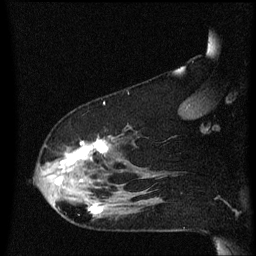
Breast MRI (dynamic contrast-enhanced), one sagittal slice. Slice 46 of 60 in the series (ordered by position). Dynamic contrast-enhanced series, image 2 of 3 at this slice position (ordered by acquisition). 1.5 T. TE 4.2 ms, TR 8.4 ms. 256 × 256 image matrix. Patient: female, 48 years.
Structures marked on this image (semi-automatically segmented with operator editing):
- analysis volume of interest (the breast-tissue region the enhancement analysis was run in; not a lesion): bounding box <34,126,134,221> (left, top, right, bottom; pixels)
- tumour enhancement mask (voxels above the 70 % enhancement threshold inside the analysis volume of interest): <56,140,109,215>